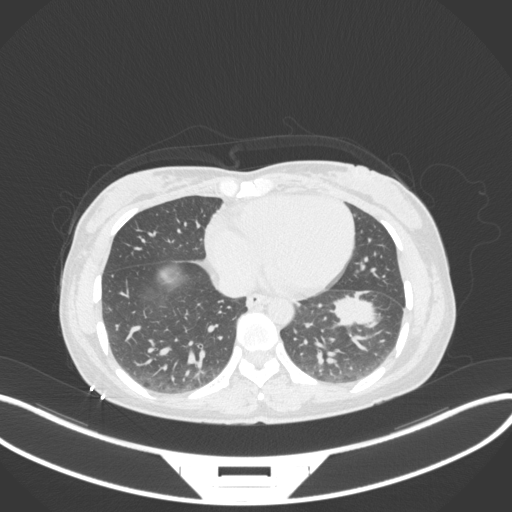
Chest CT, one axial slice; slice 124 of 361 in the series (ordered by position); reconstruction kernel B31f; lung window (W 1500 / L -600 HU); 1 mm slice thickness; 512 × 512 image matrix. Patient: female, 41 years. Case-level facts recorded for this patient, not image findings: clinical TNM (as recorded): T2a N3 M1b.
Structures marked on this image (rectangle marked by the reading radiologist):
- lung tumour (recorded histology: adenocarcinoma): bounding box [x1, y1, x2, y2] px = [333, 288, 387, 337]